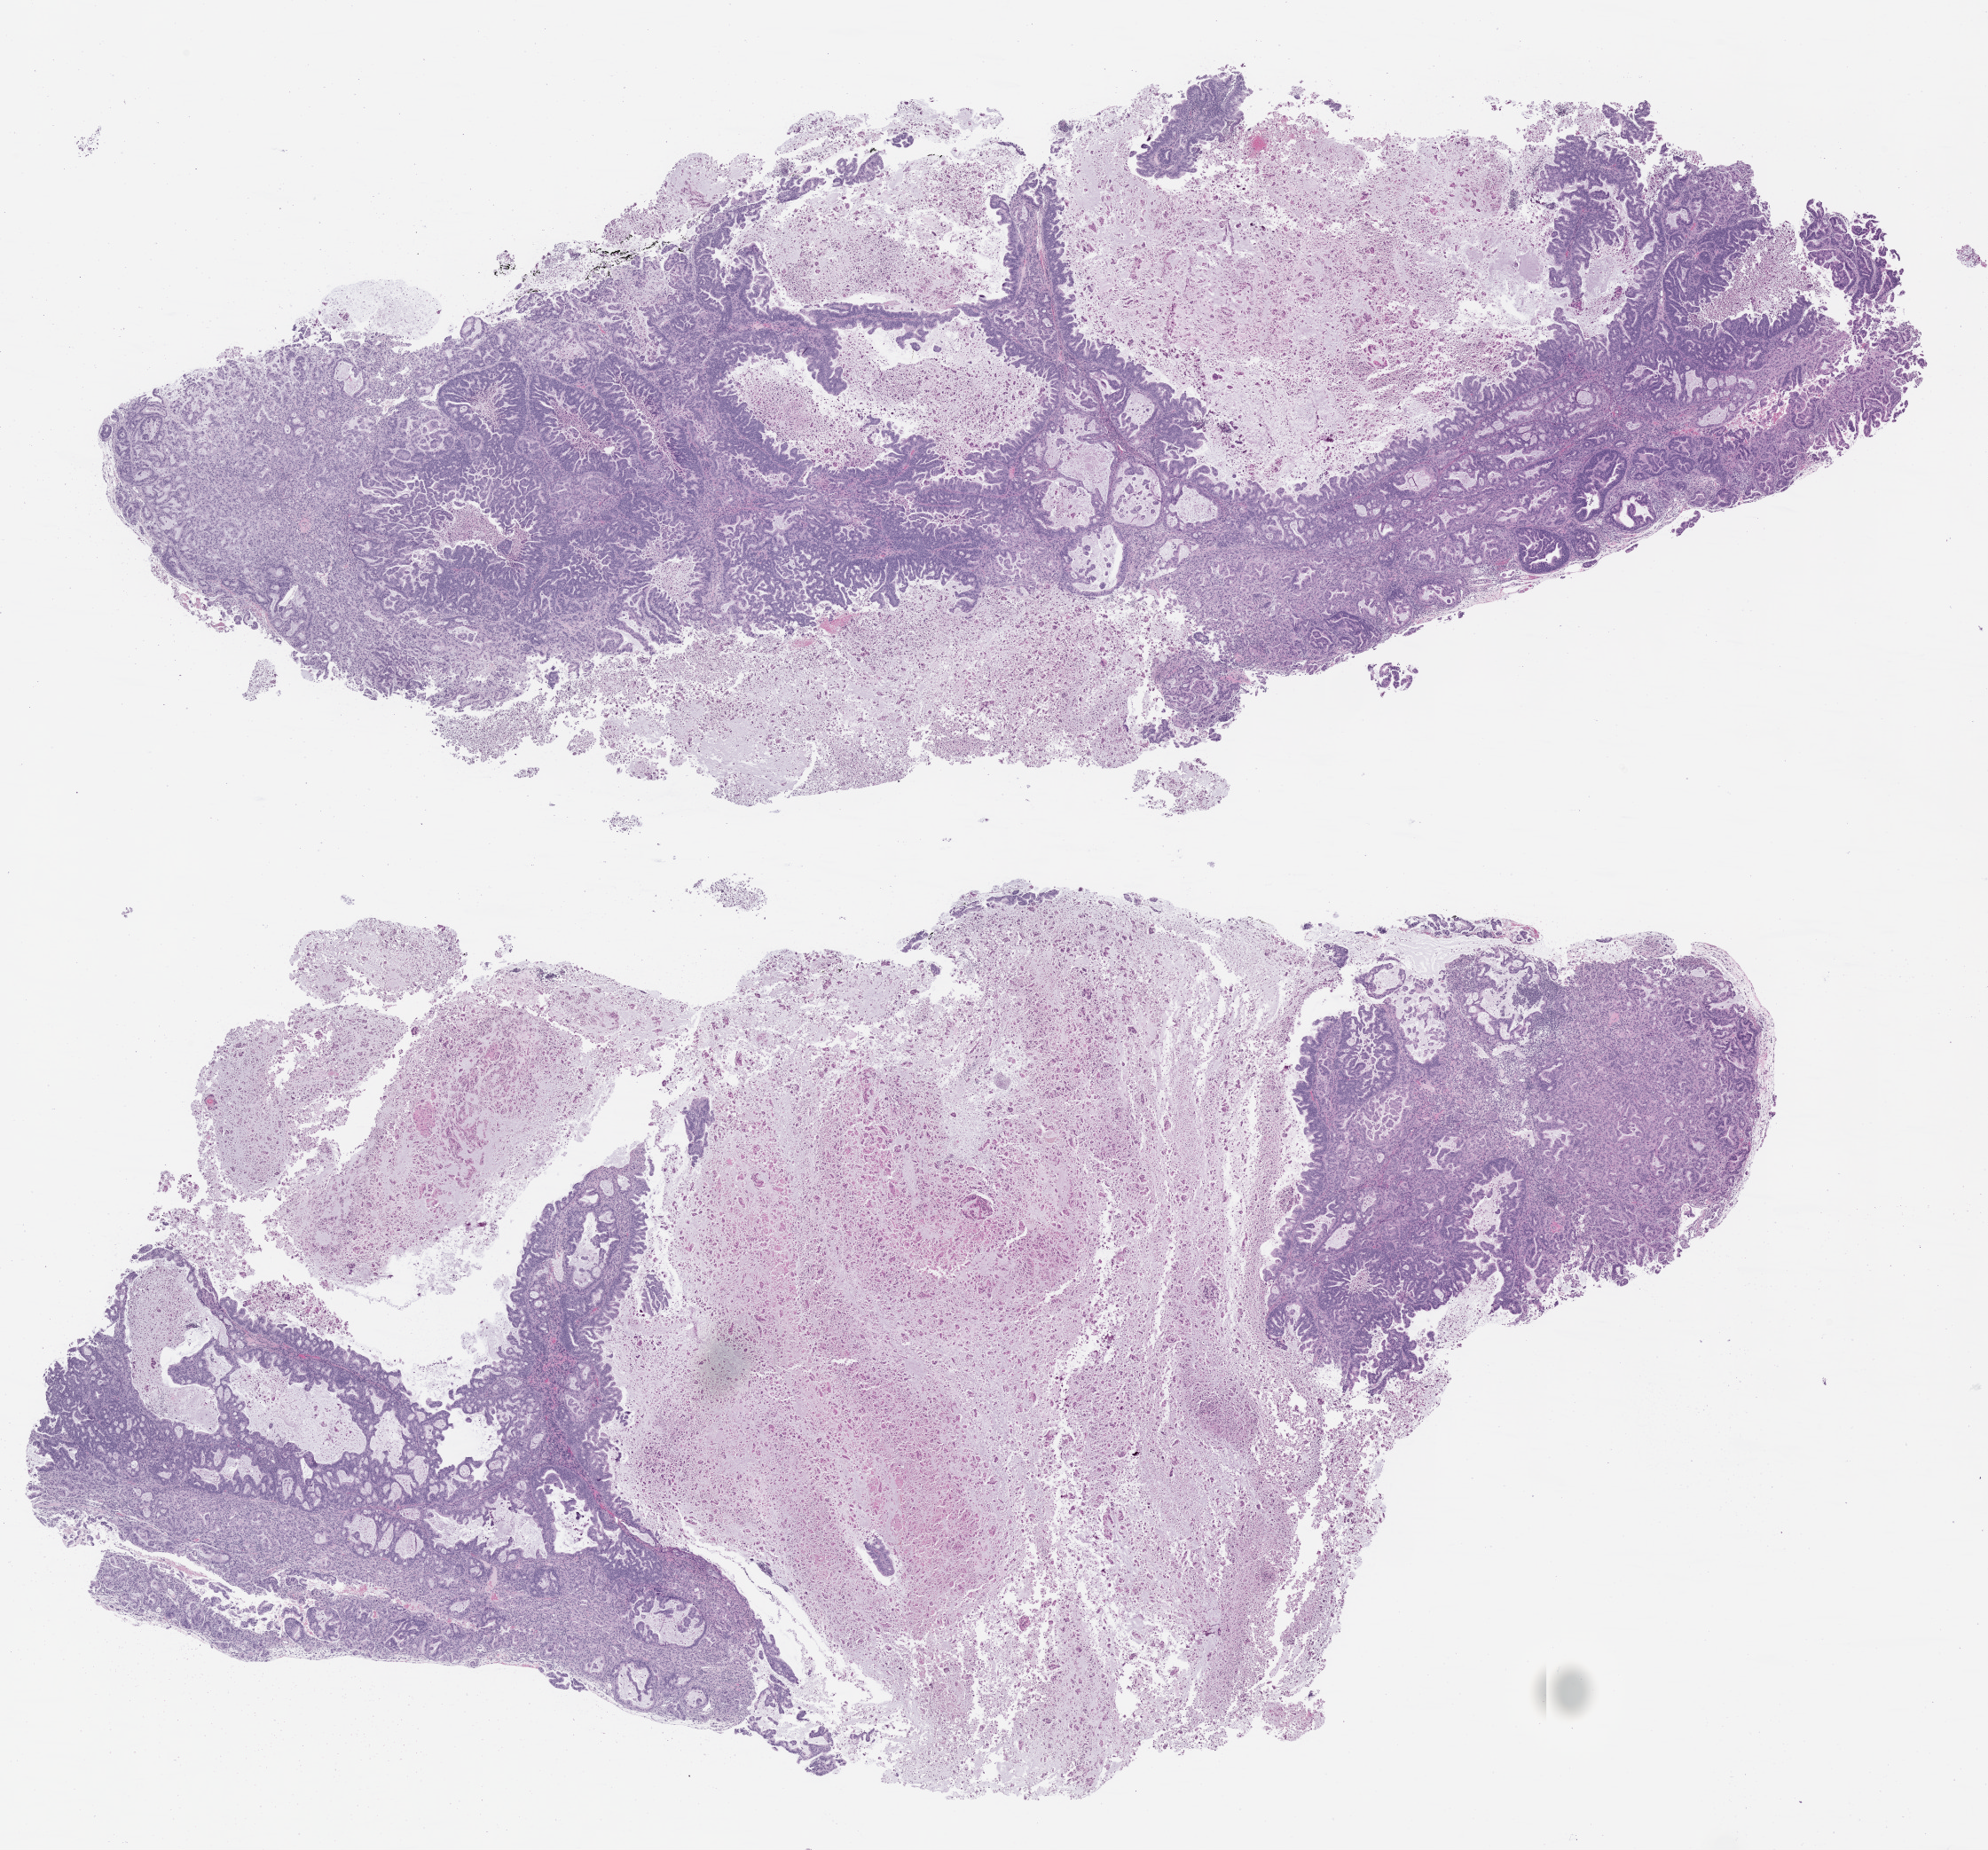
Whole-slide image, haematoxylin and eosin: patient-derived xenograft (human tumor grown in a mouse), passage 0, a low-resolution overview of the entire scanned area, about 18.0 x 16.8 mm, formalin-fixed, paraffin-embedded (FFPE) tissue, originating tumor site category: pancreas.
- originating patient diagnosis: Pancreatic Adenocarcinoma